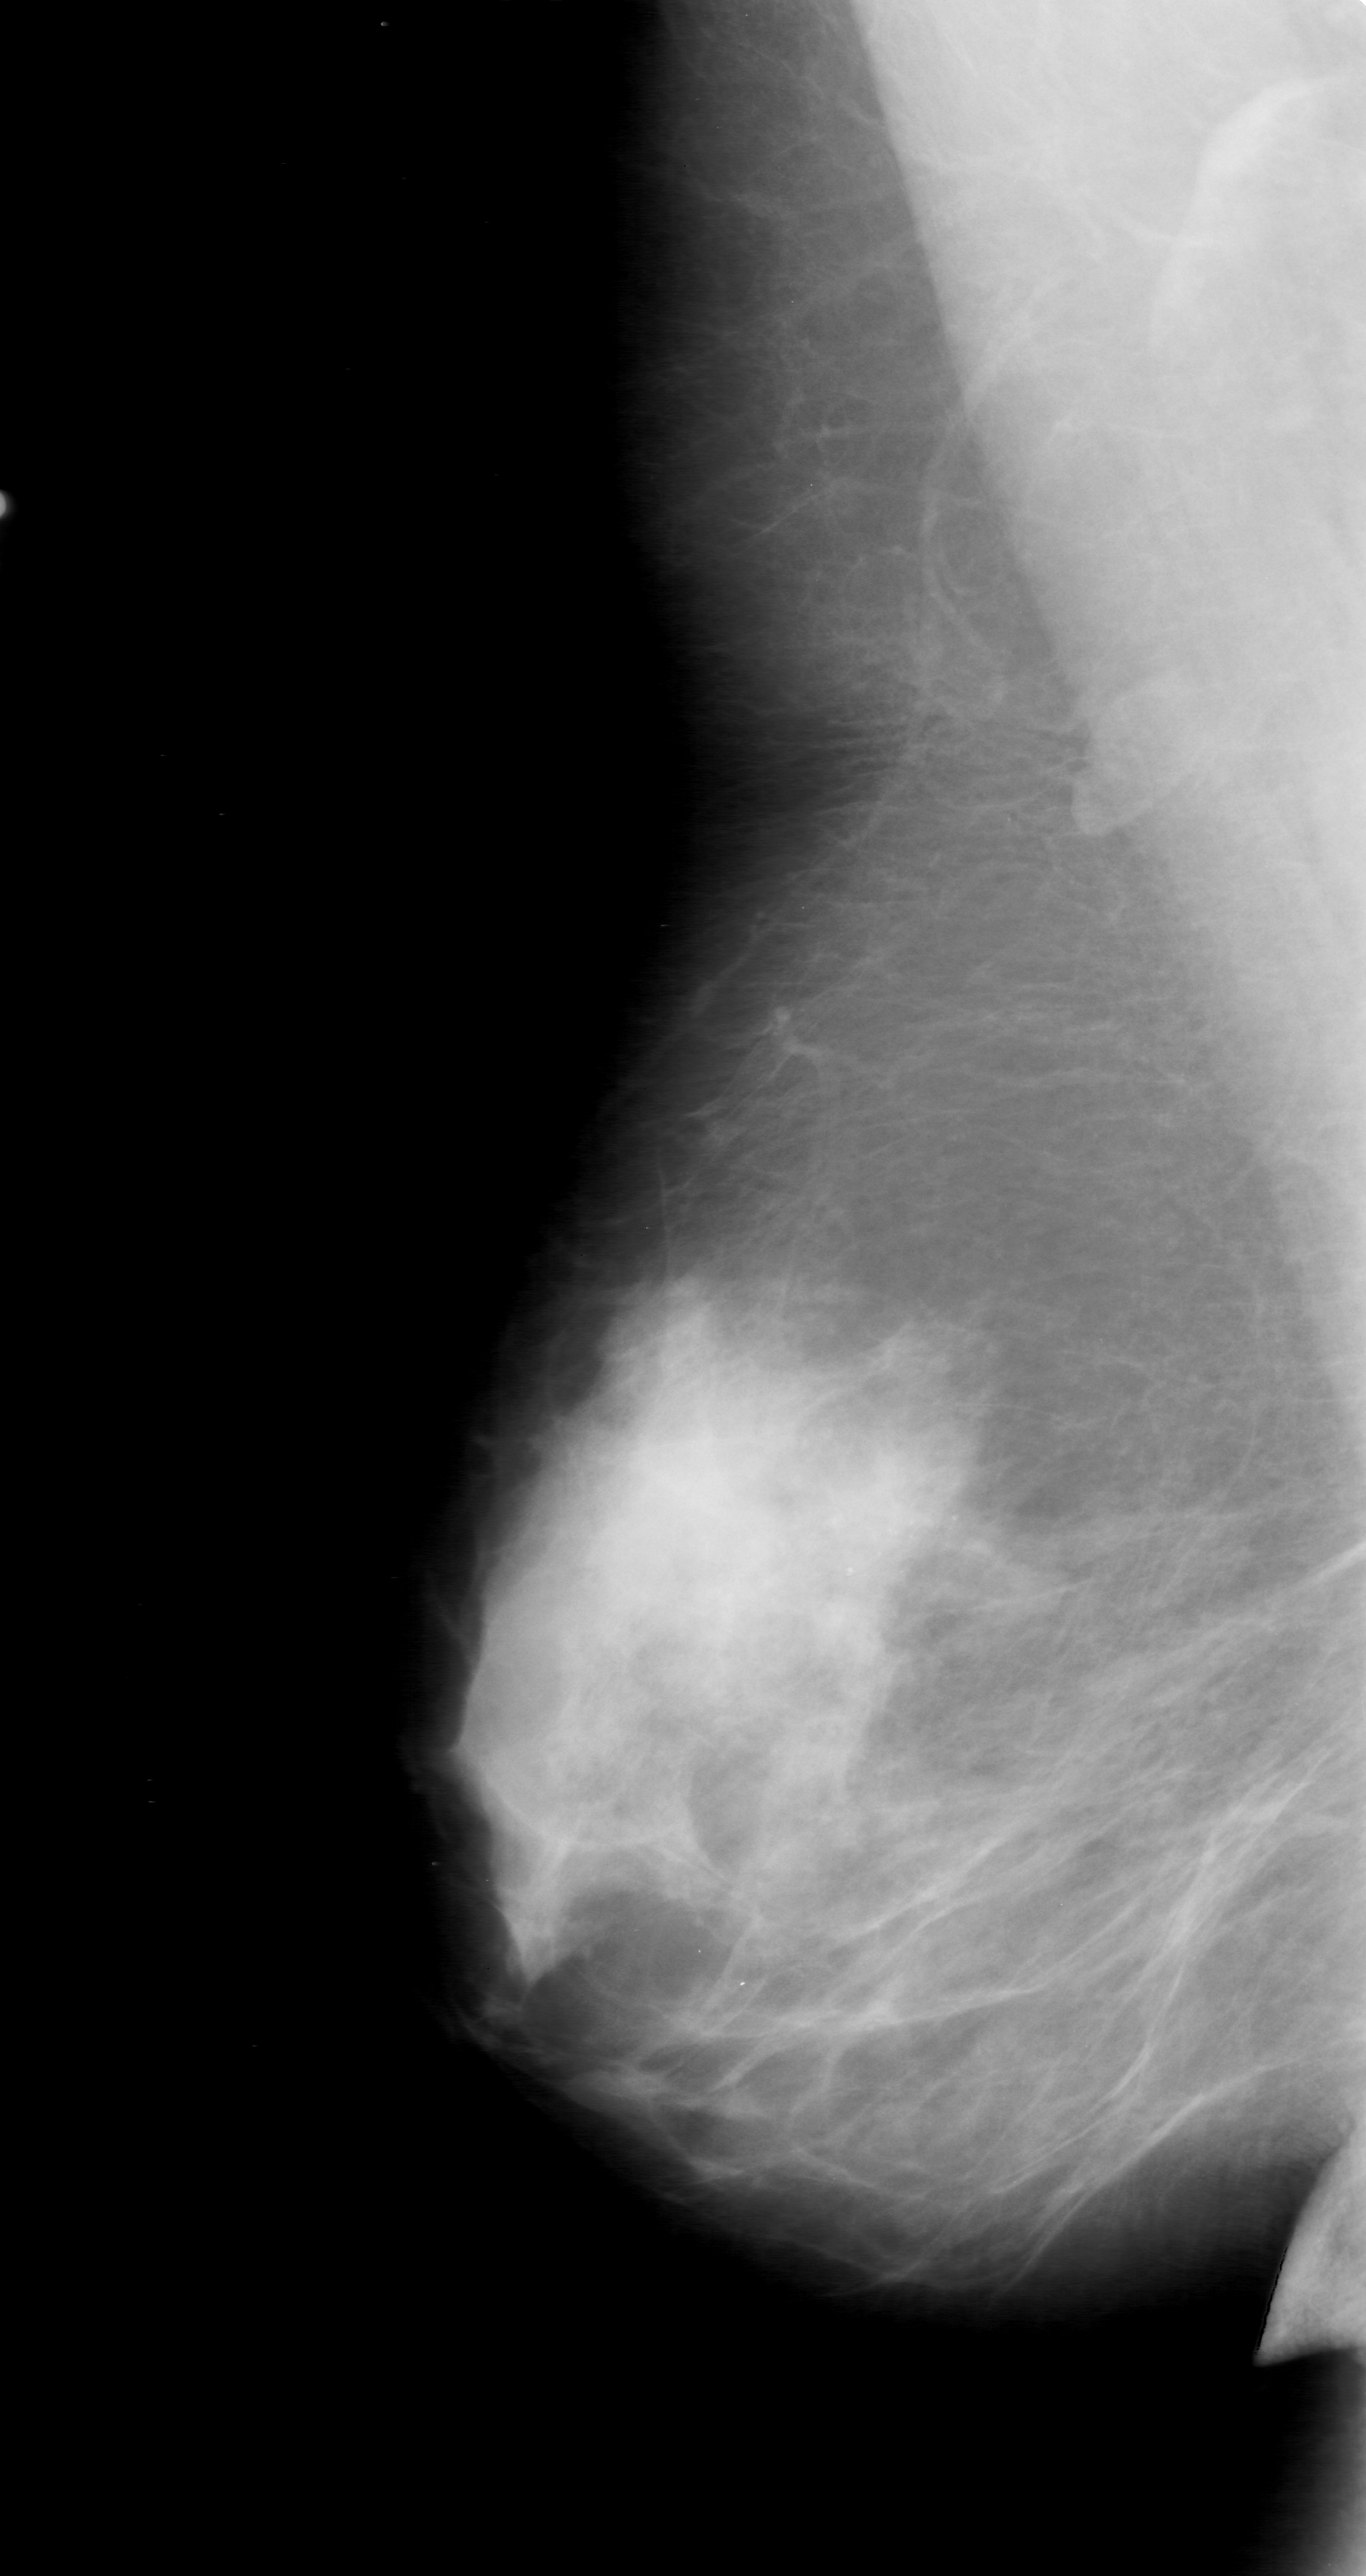
Digitized screen-film mammogram; right breast; MLO view; breast composition: heterogeneously dense (BI-RADS density category 3 of 4).
Radiologist-marked abnormalities on this image: calcifications, morphology pleomorphic, distribution clustered; BI-RADS assessment category 0 (incomplete: needs additional imaging); pathology (as recorded): malignant.